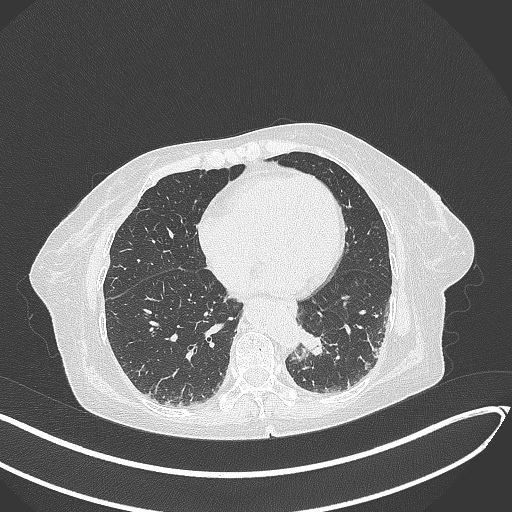
Chest CT, one axial slice. Slice 72 of 324 in the series (ordered by position). Reconstruction kernel B70f. 120 kVp. Lung window (W 1500 / L -600 HU). 1 mm slice thickness. 512 × 512 image matrix, field of view 400 × 400 mm. Female patient, age 82 years. Case-level facts recorded for this patient, not image findings: clinical TNM (as recorded): T1b N0 M1.
Annotated regions visible in this slice (bounding box drawn by a radiologist):
- lung tumour (recorded histology: adenocarcinoma): bounding box (x1, y1, x2, y2) in pixels: (294, 321, 331, 364)